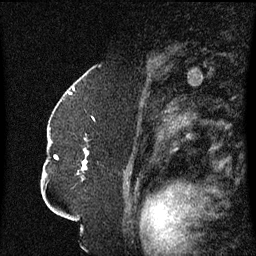
Breast MRI (dynamic contrast-enhanced), one sagittal slice; position 42 of 60 along the scan axis; dynamic contrast-enhanced series, image 2 of 3 at this slice position (ordered by acquisition); 1.5 T; TE 4.2 ms, TR 8.4 ms; 2.3 mm slice thickness; 256 × 256 image matrix. Patient: female, 52 years. Case-level facts recorded for this patient, not image findings: setting: breast cancer imaged before/during neoadjuvant chemotherapy; receptor status: HR-positive, HER2-negative.
Annotated regions visible in this slice (semi-automatic segmentation, software-assisted and operator-edited):
- analysis volume of interest (the breast-tissue region the enhancement analysis was run in; not a lesion): bounding box <49,124,89,181> (left, top, right, bottom; pixels)
- tumour enhancement mask (voxels above the 70 % enhancement threshold inside the analysis volume of interest): <56,150,88,175>